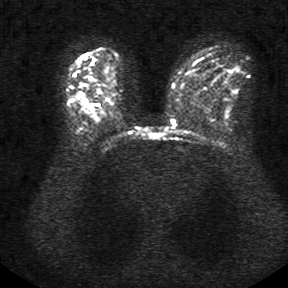
Breast MRI, one axial slice; slice 24 of 34 in the series (ordered by position); diffusion-weighted series; image 2 of 4 stored at this slice position (different b-values; order by instance number); 1.5 T; 5 mm slice thickness; 288 × 288 image matrix. Female patient.
Annotated regions visible in this slice (outlined manually by an expert reader):
- tumour on diffusion-weighted imaging: box from (x=83, y=97) to (x=93, y=110) px